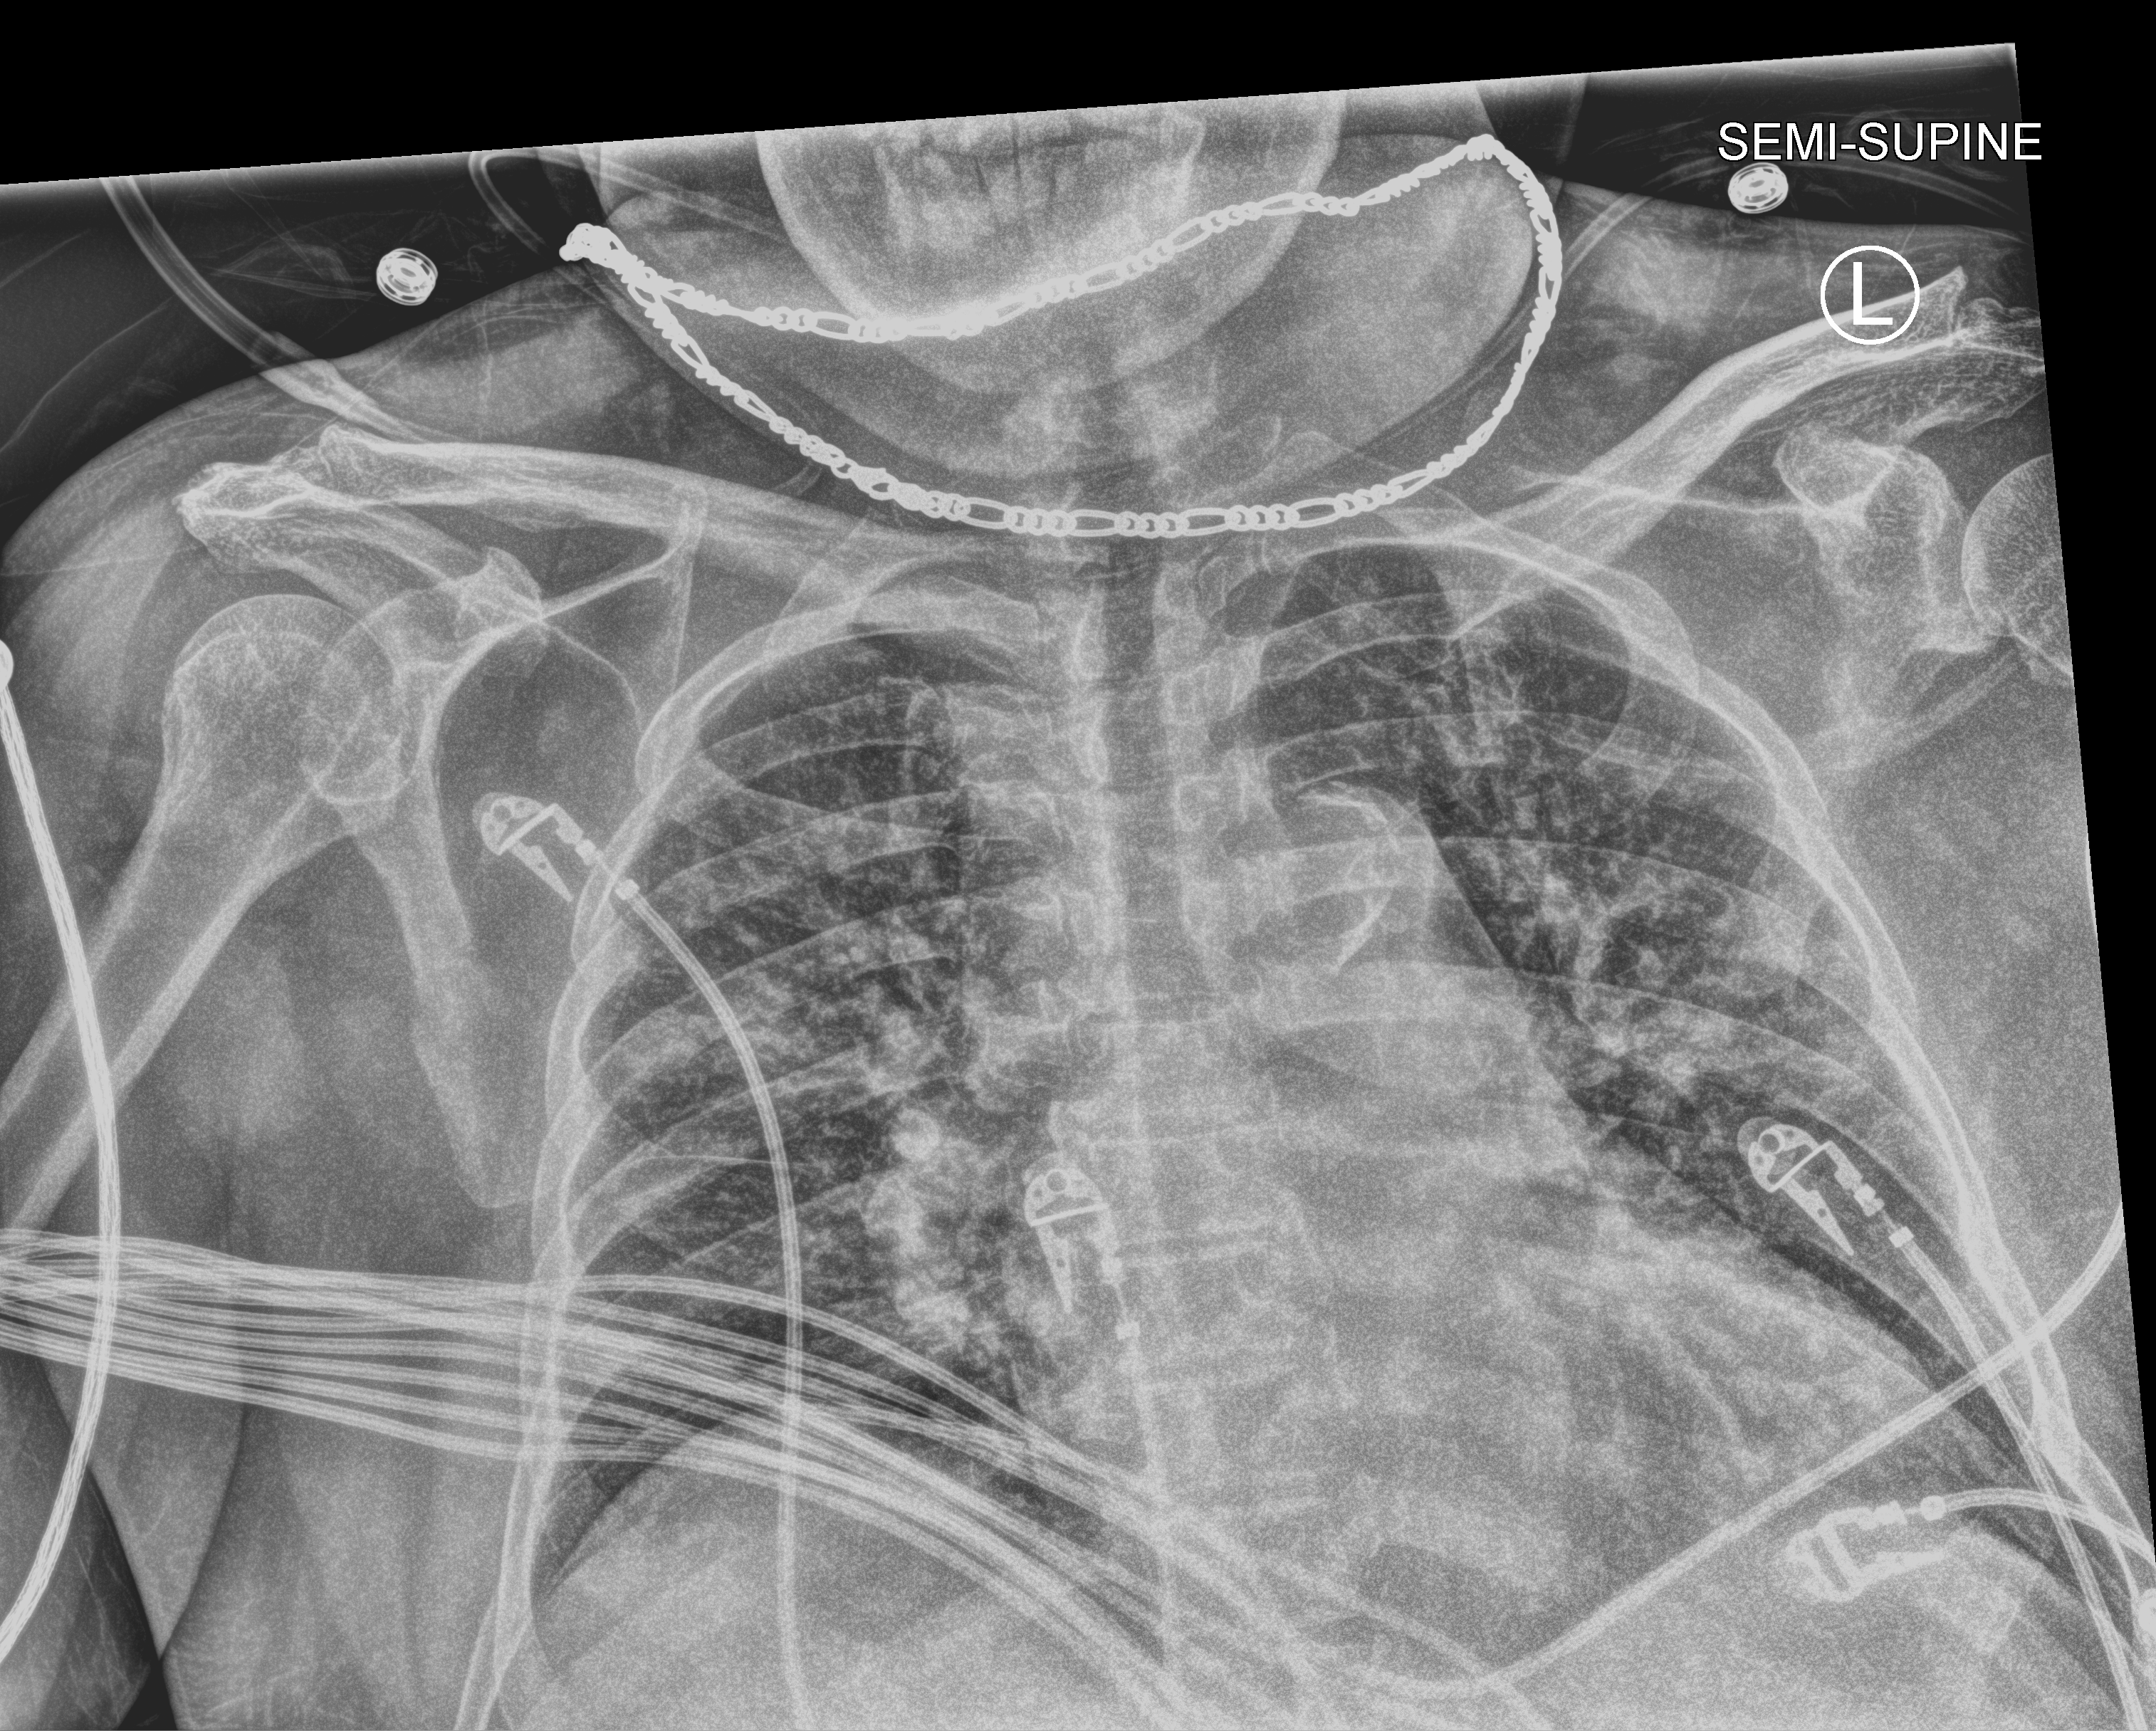
Chest X-ray (portable), anteroposterior (AP) projection. Male patient hospitalised with COVID-19, age 60–74 years.
Admission-level facts for this patient (not findings on this image; timing relative to this image not recorded):
- admitted to intensive care during this hospital stay: yes